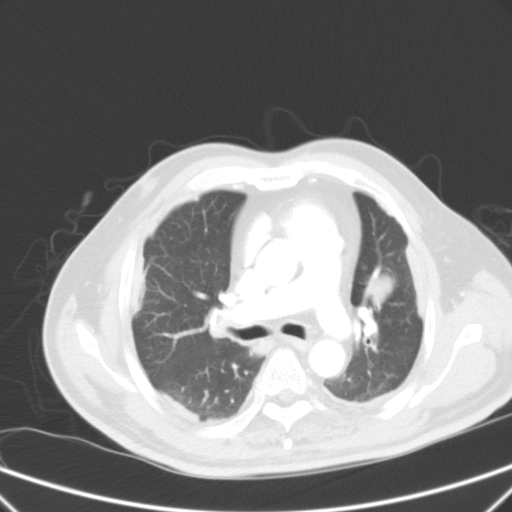
Chest CT, one axial slice; position 38 of 59 along the scan axis; 120 kVp; intravenous contrast given; lung window (W 1500 / L -600 HU); 5 mm slice thickness; 512 × 512 image matrix, field of view 357 × 357 mm. Patient: male, 66 years. From the clinical record (not read from this slice): clinical TNM (as recorded): T1c N3 M1a.
Structures marked on this image (bounding box drawn by a radiologist):
- lung tumour (recorded histology: squamous cell carcinoma): box from (x=358, y=265) to (x=399, y=311) px